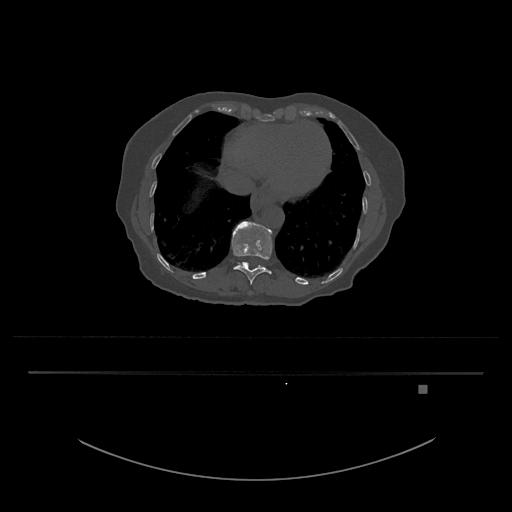
CT including the spine, one axial slice; position 658 of 797 along the scan axis; reconstruction kernel Br40s/3; 120 kVp; bone window (W 1800 / L 400 HU); 0.5 mm slice thickness; 512 × 512 image matrix. Female patient, age 57 years. Case-level facts recorded for this patient, not image findings: primary cancer: cervical.
Structures marked on this image (semi-automatic segmentation, software-assisted and operator-edited):
- T11 vertebra: bounding box <231,221,273,285> (left, top, right, bottom; pixels)
- T12 vertebra: <237,262,266,269>